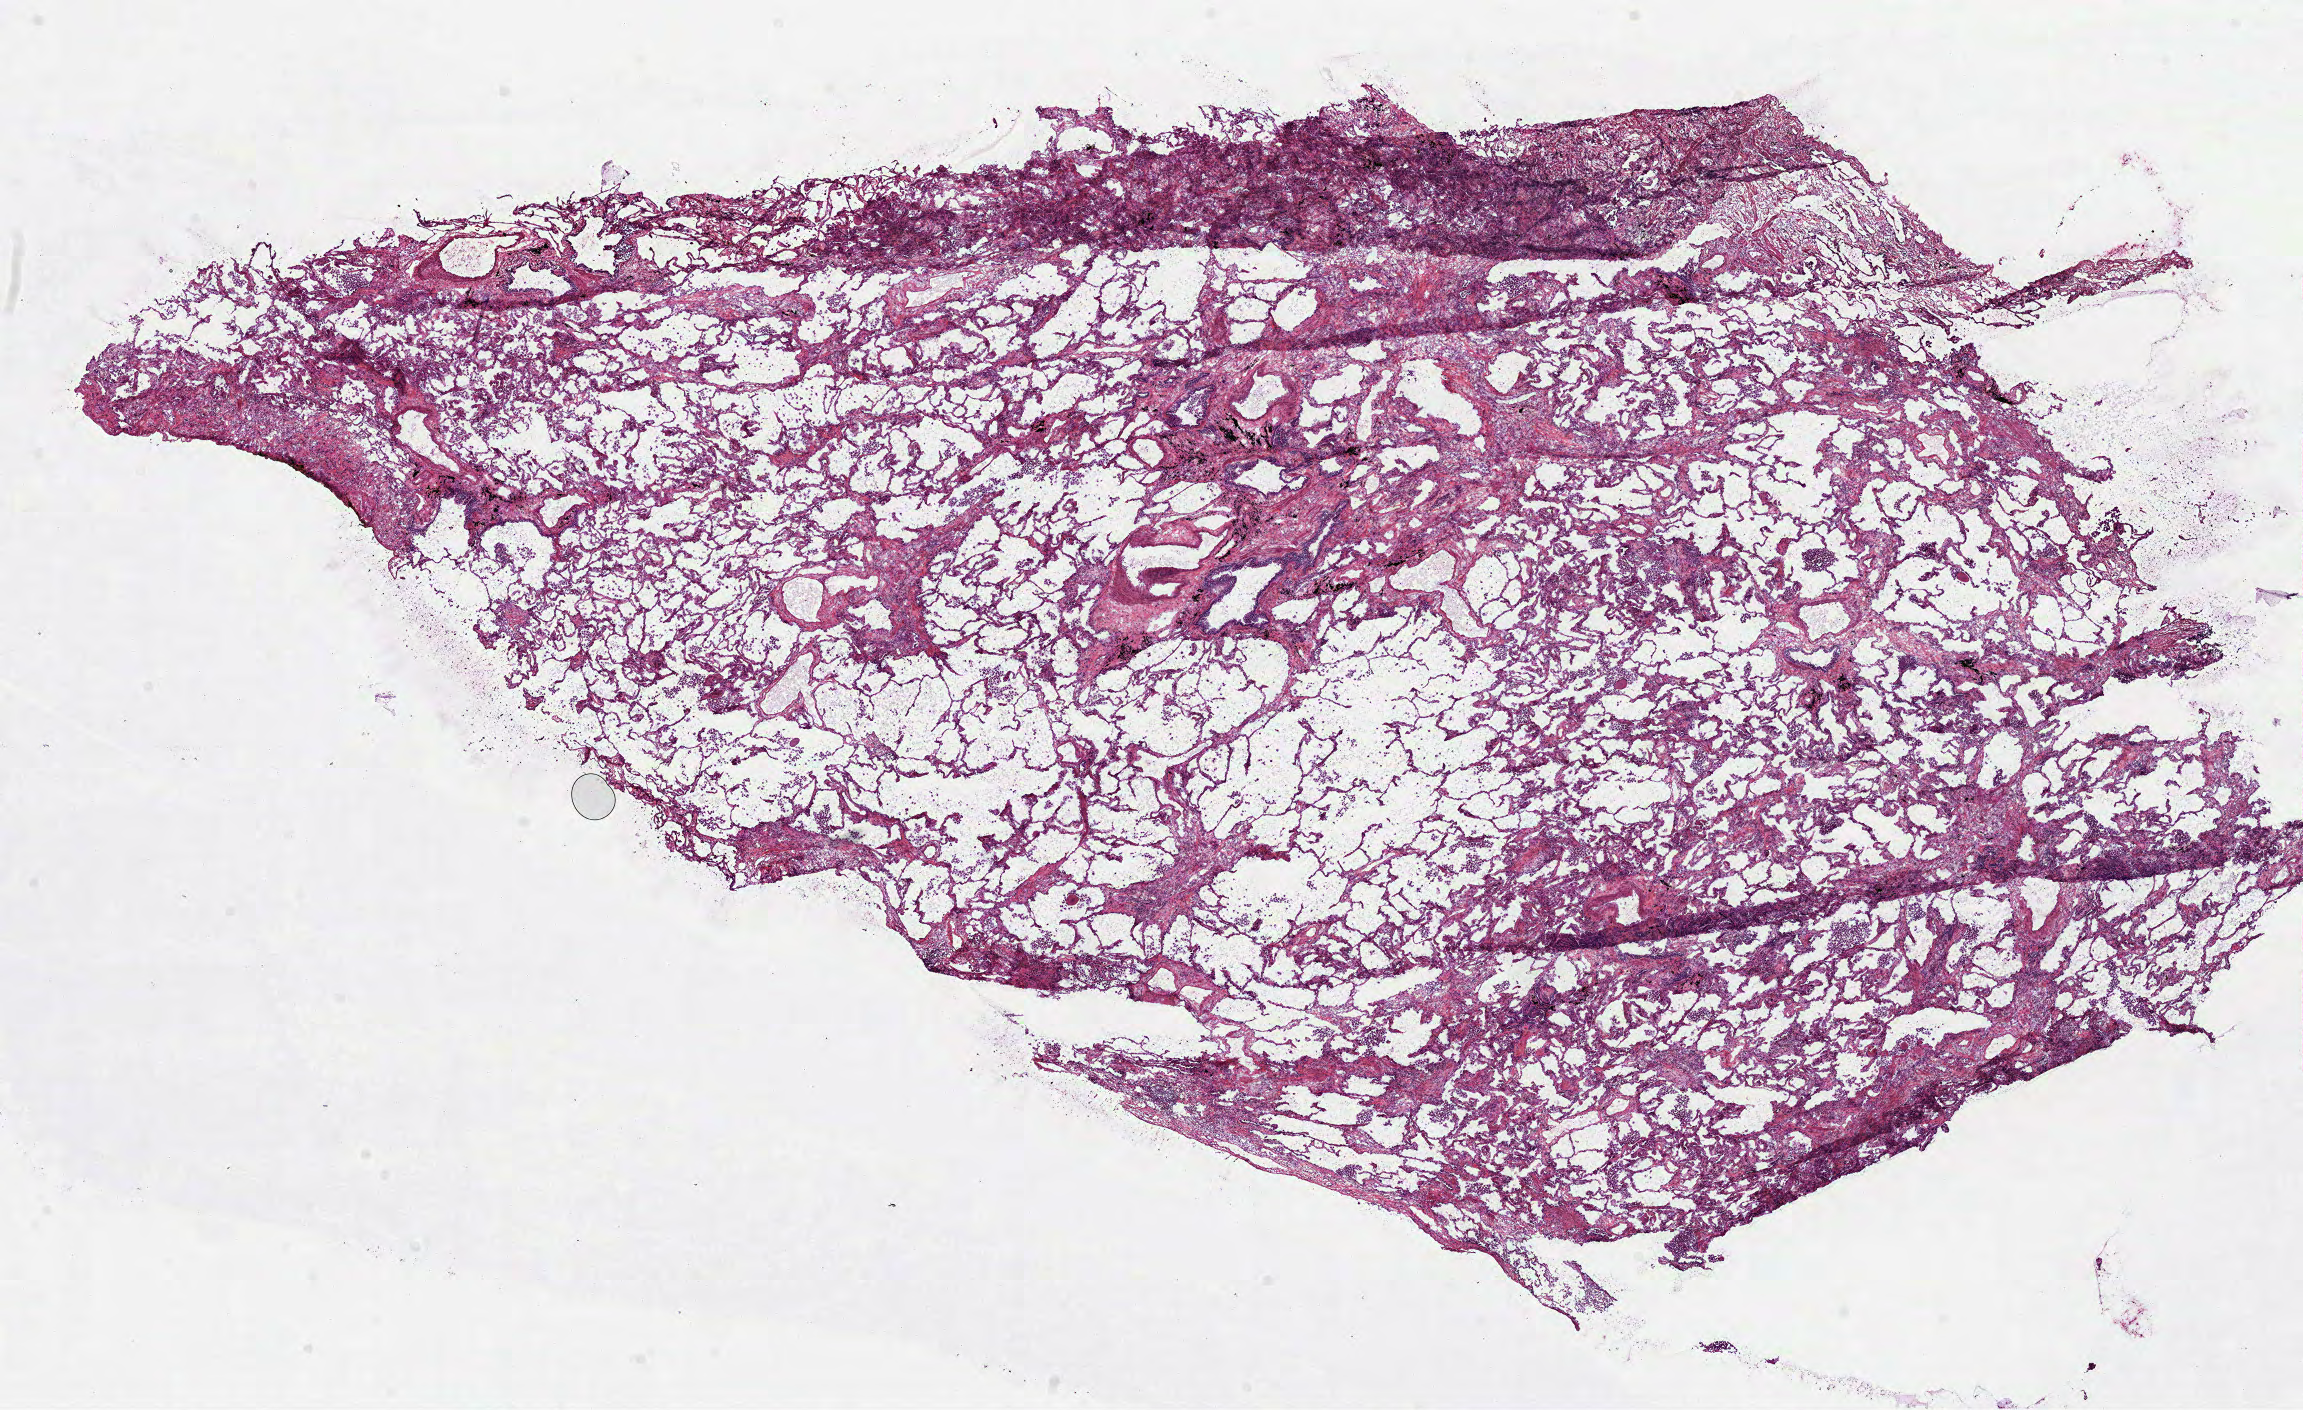
Digitized Hematoxylin and eosin (H&E) stained tissue section (whole slide), low-resolution overview of the scanned area, about 18.6 x 11.4 mm; frozen section from the top of the tissue portion; lung, solid tissue normal (non-tumour tissue) sample. Female, age 84 years at initial diagnosis.
This section: solid tissue normal (non-tumour) sample from the same patient. Patient diagnosis: Adenocarcinoma, NOS (upper lobe, lung).